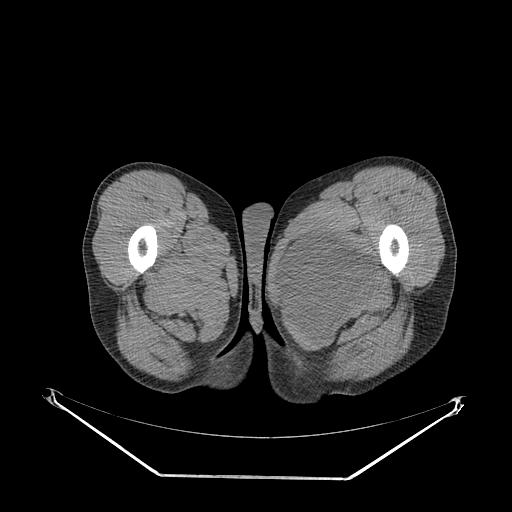
CT of an extremity soft-tissue mass (from a PET/CT study), one axial slice. Slice 34 of 267 in the series (ordered by position). Reconstruction kernel SOFT. 140 kVp. Soft-tissue window (W 400 / L 40 HU). 3.75 mm slice thickness. 512 × 512 image matrix, field of view 500 × 500 mm. Male patient. Case-level facts recorded for this patient, not image findings: histological type: pleiomorphic liposarcoma; grade: high; site of the primary tumour: left thigh.
Annotated regions visible in this slice (expert contour drawn on MRI and transferred to this co-registered scan by the dataset authors):
- gross tumour volume including surrounding oedema: bounding box (x1, y1, x2, y2) in pixels: (283, 231, 373, 325)
- gross tumour volume (mass): (283, 233, 371, 316)